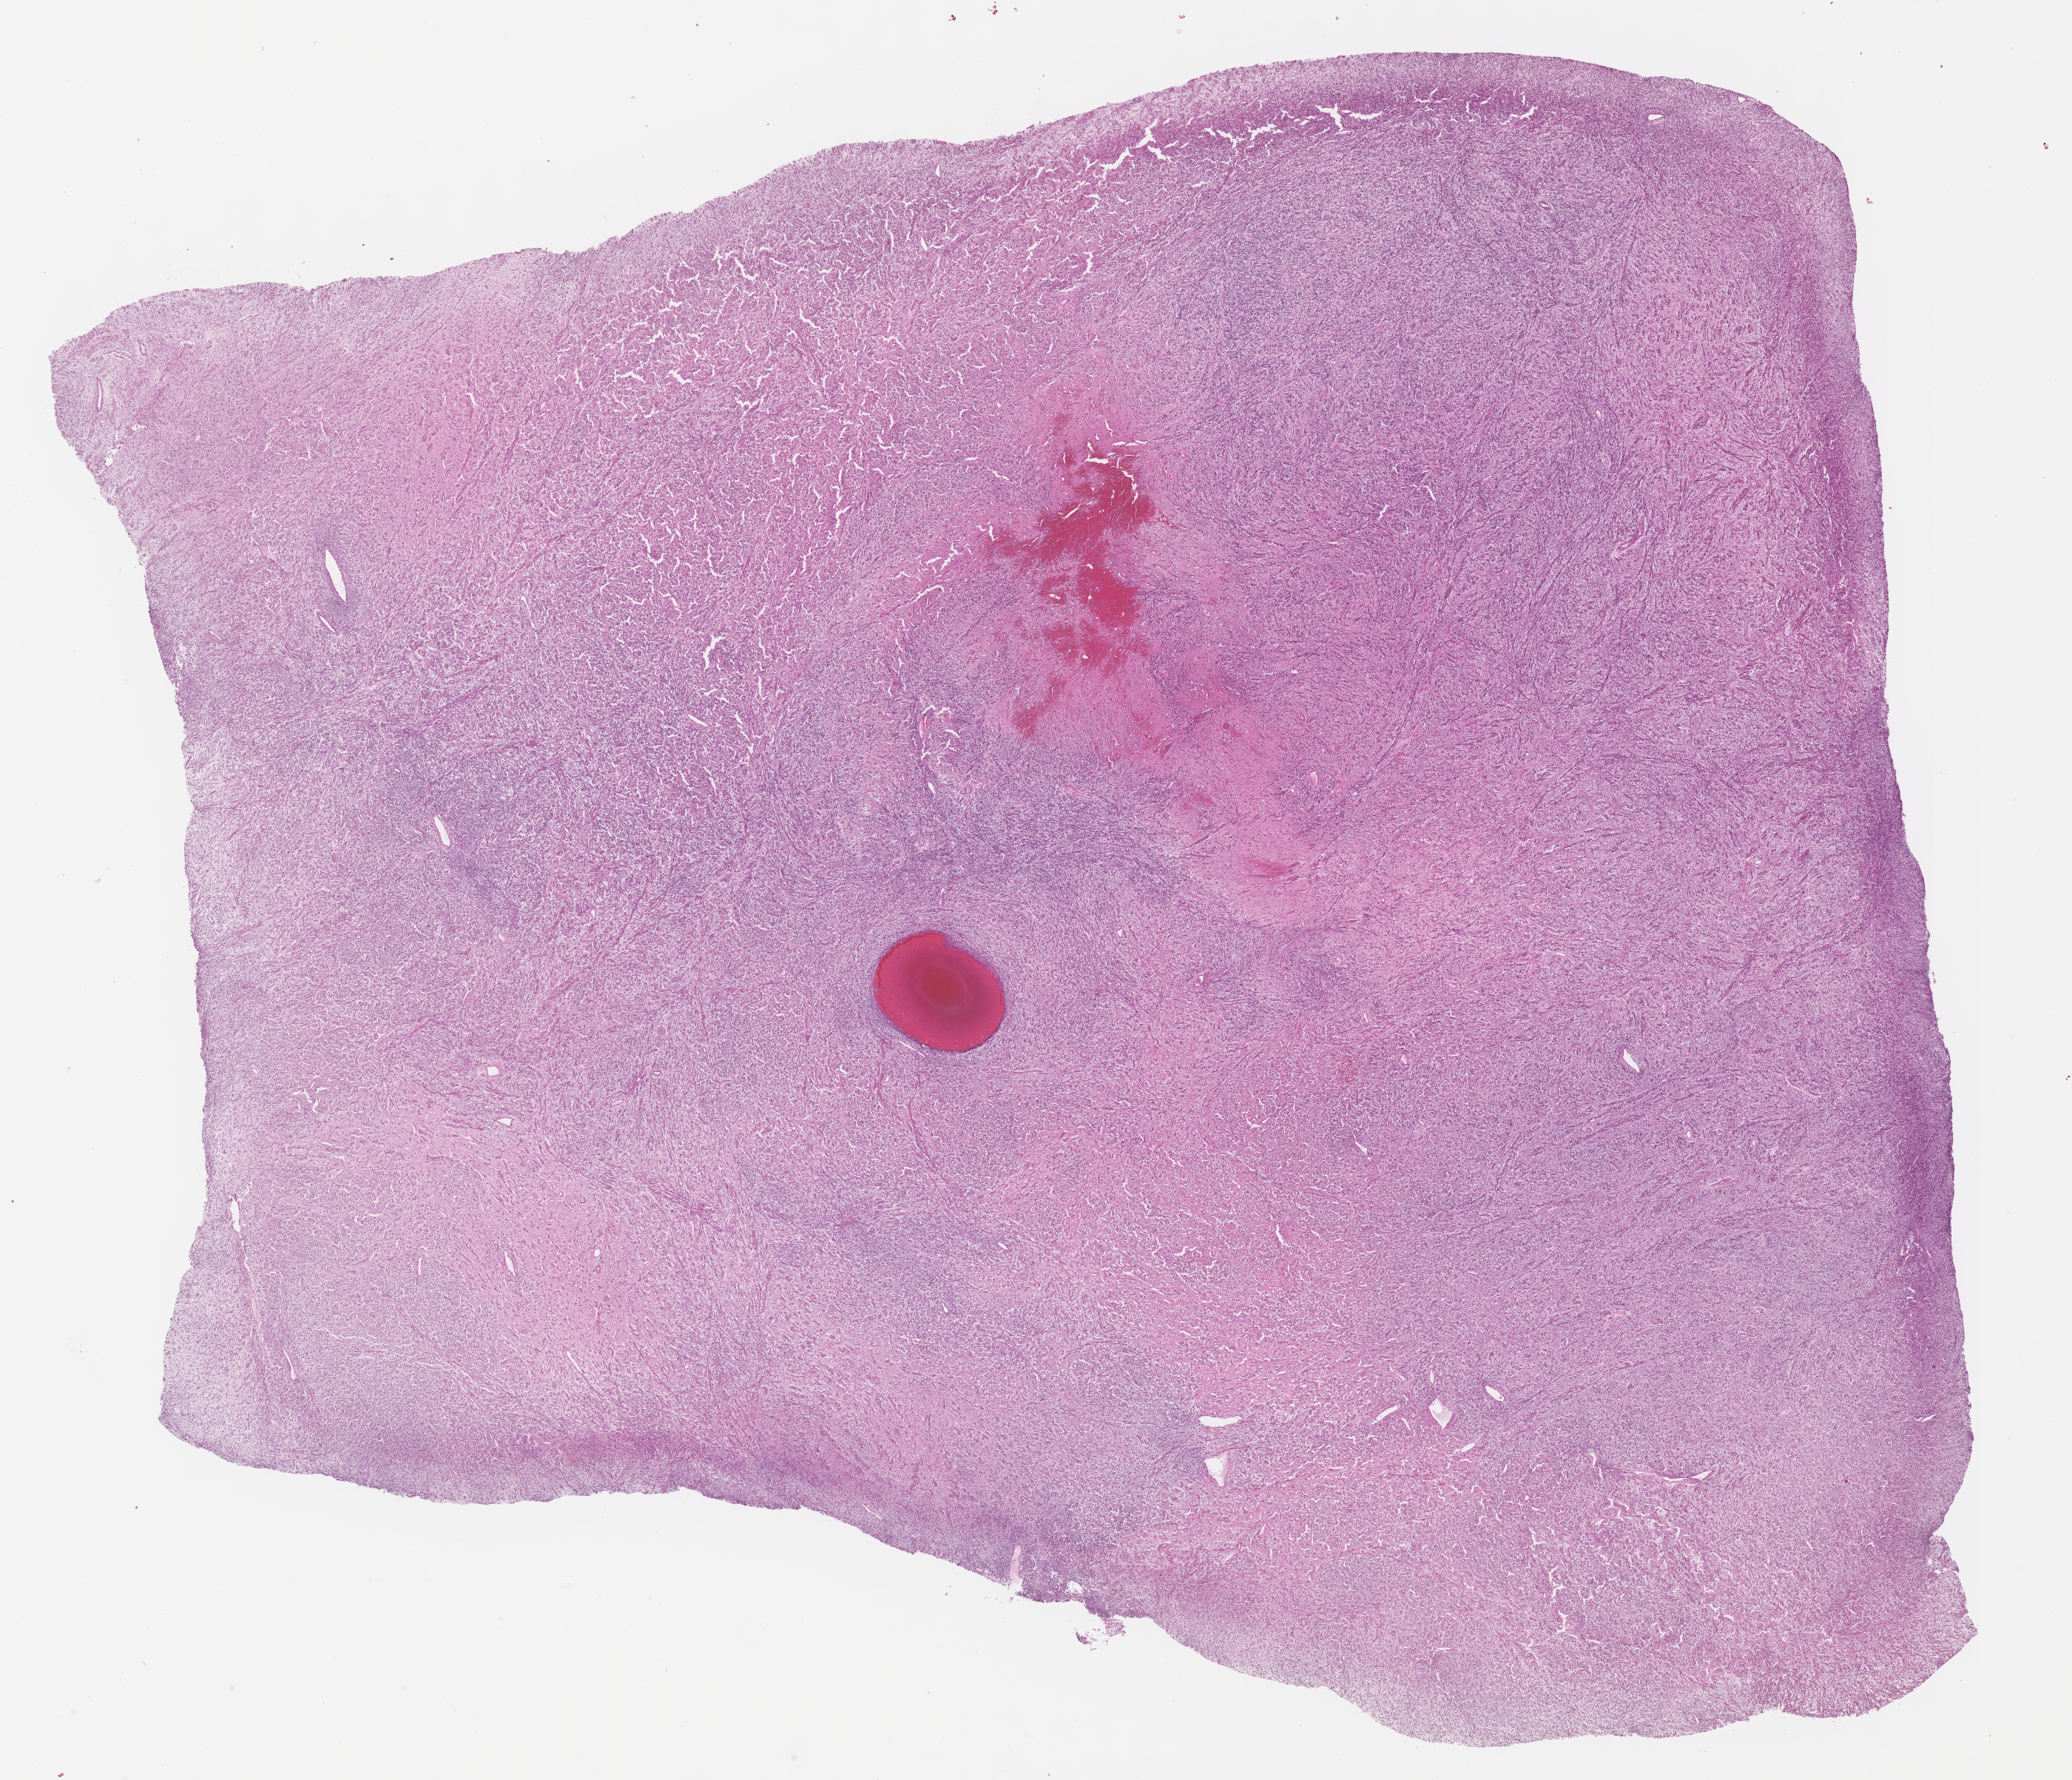
H&E whole-slide image of tumor tissue — low-resolution overview of the scanned area, about 22.6 x 19.4 mm; formalin-fixed, paraffin-embedded (FFPE) tissue; site: pelvis. Male patient, age at diagnosis 16.2 years.
Diagnosis: rhabdomyosarcoma; histological classification: embryonal rhabdomyosarcoma. Metastatic status at presentation (as recorded): non-metastatic (unconfirmed).